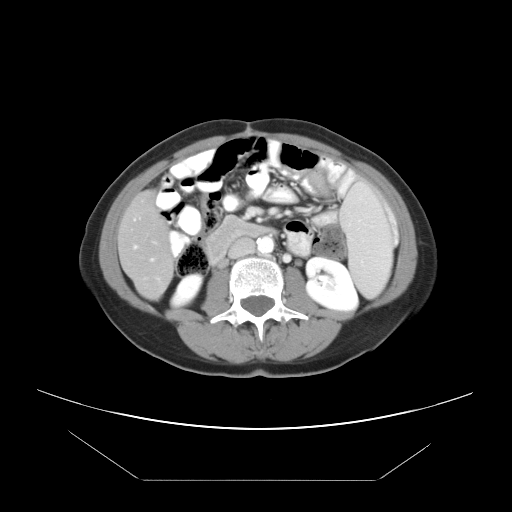
Contrast-enhanced abdominal CT, one axial slice; position 12 of 45 along the scan axis; intravenous contrast given; soft-tissue window (W 400 / L 40 HU); 512 × 512 image matrix. Female patient, age 52 years. Case-level facts recorded for this patient, not image findings: diagnosis: colorectal cancer liver metastases, imaged before liver resection; multiple liver metastases: yes.
Structures marked on this image (outlined manually by an expert reader):
- hepatic veins: bounding box <134,246,137,249> (left, top, right, bottom; pixels)
- liver: <119,194,173,299>
- planned liver remnant (the part of the liver to remain after resection): <119,194,167,250>
- portal vein (with intrahepatic branches): <150,258,155,262>